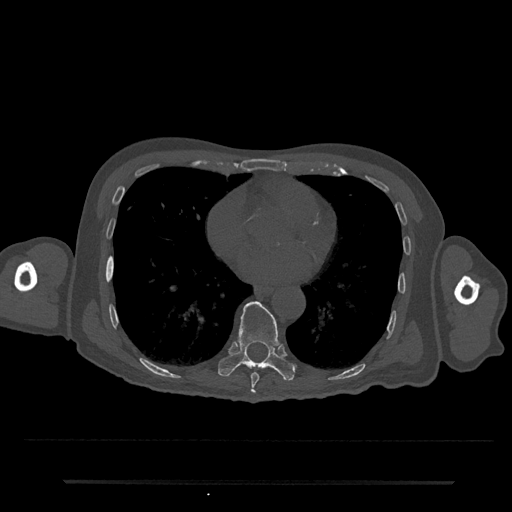
CT including the spine, one axial slice. Position 381 of 797 along the scan axis. Reconstruction kernel Br40s/3. Bone window (W 1800 / L 400 HU). 0.5 mm slice thickness. 512 × 512 image matrix, field of view 427 × 427 mm. Patient: male, 74 years. From the clinical record (not read from this slice): primary cancer: prostate.
Outlined on this slice (semi-automatically segmented with operator editing):
- T8 vertebra: bounding box [x1, y1, x2, y2] px = [251, 373, 259, 394]
- T9 vertebra: [218, 301, 295, 381]